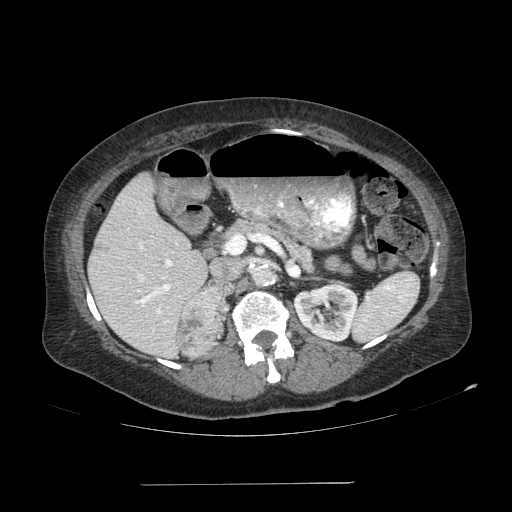
Contrast-enhanced abdominal CT, one axial slice; reconstruction kernel SOFT; soft-tissue window (W 400 / L 40 HU); 512 × 512 image matrix, field of view 440 × 440 mm. Patient: female, 67 years. Case-level facts recorded for this patient, not image findings: diagnosis: adrenocortical carcinoma; tumour side: right adrenal; tumour size at pathology: 9.8 cm; Ki-67 index: 59 %; stage (as recorded): 4.
Outlined on this slice (semi-automatically segmented with operator editing):
- mass: bounding box (x1, y1, x2, y2) in pixels: (178, 285, 224, 358)